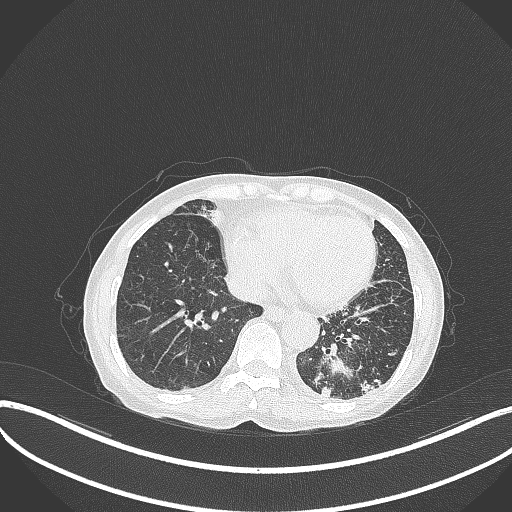
Chest CT, one axial slice. Position 88 of 370 along the scan axis. Lung window (W 1500 / L -600 HU). 512 × 512 image matrix, field of view 400 × 400 mm. Patient: female, 78 years. Case-level facts recorded for this patient, not image findings: clinical TNM (as recorded): T3 N0 M1.
Annotated regions visible in this slice (rectangle marked by the reading radiologist):
- lung tumour (recorded histology: squamous cell carcinoma): bounding box (x1, y1, x2, y2) in pixels: (307, 337, 363, 404)